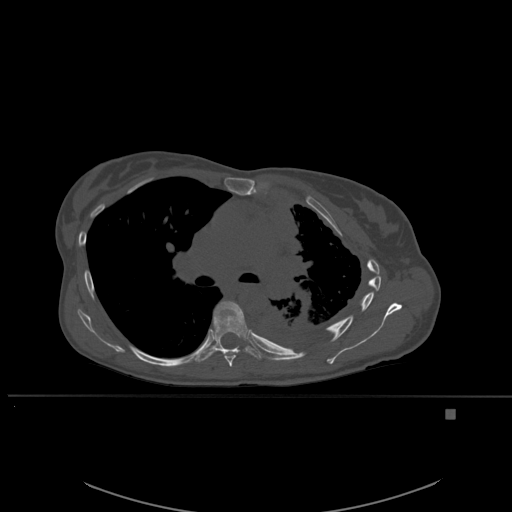
CT including the spine, one axial slice; slice 374 of 537 in the series (ordered by position); bone window (W 1800 / L 400 HU); 1.5 mm slice thickness; 512 × 512 image matrix, field of view 440 × 440 mm. Patient: female, 45 years. From the clinical record (not read from this slice): primary cancer: lung.
Annotated regions visible in this slice (semi-automatic segmentation, software-assisted and operator-edited):
- T6 vertebra: box from (x=216, y=301) to (x=241, y=367) px
- T7 vertebra: (x=197, y=301)–(x=267, y=362)